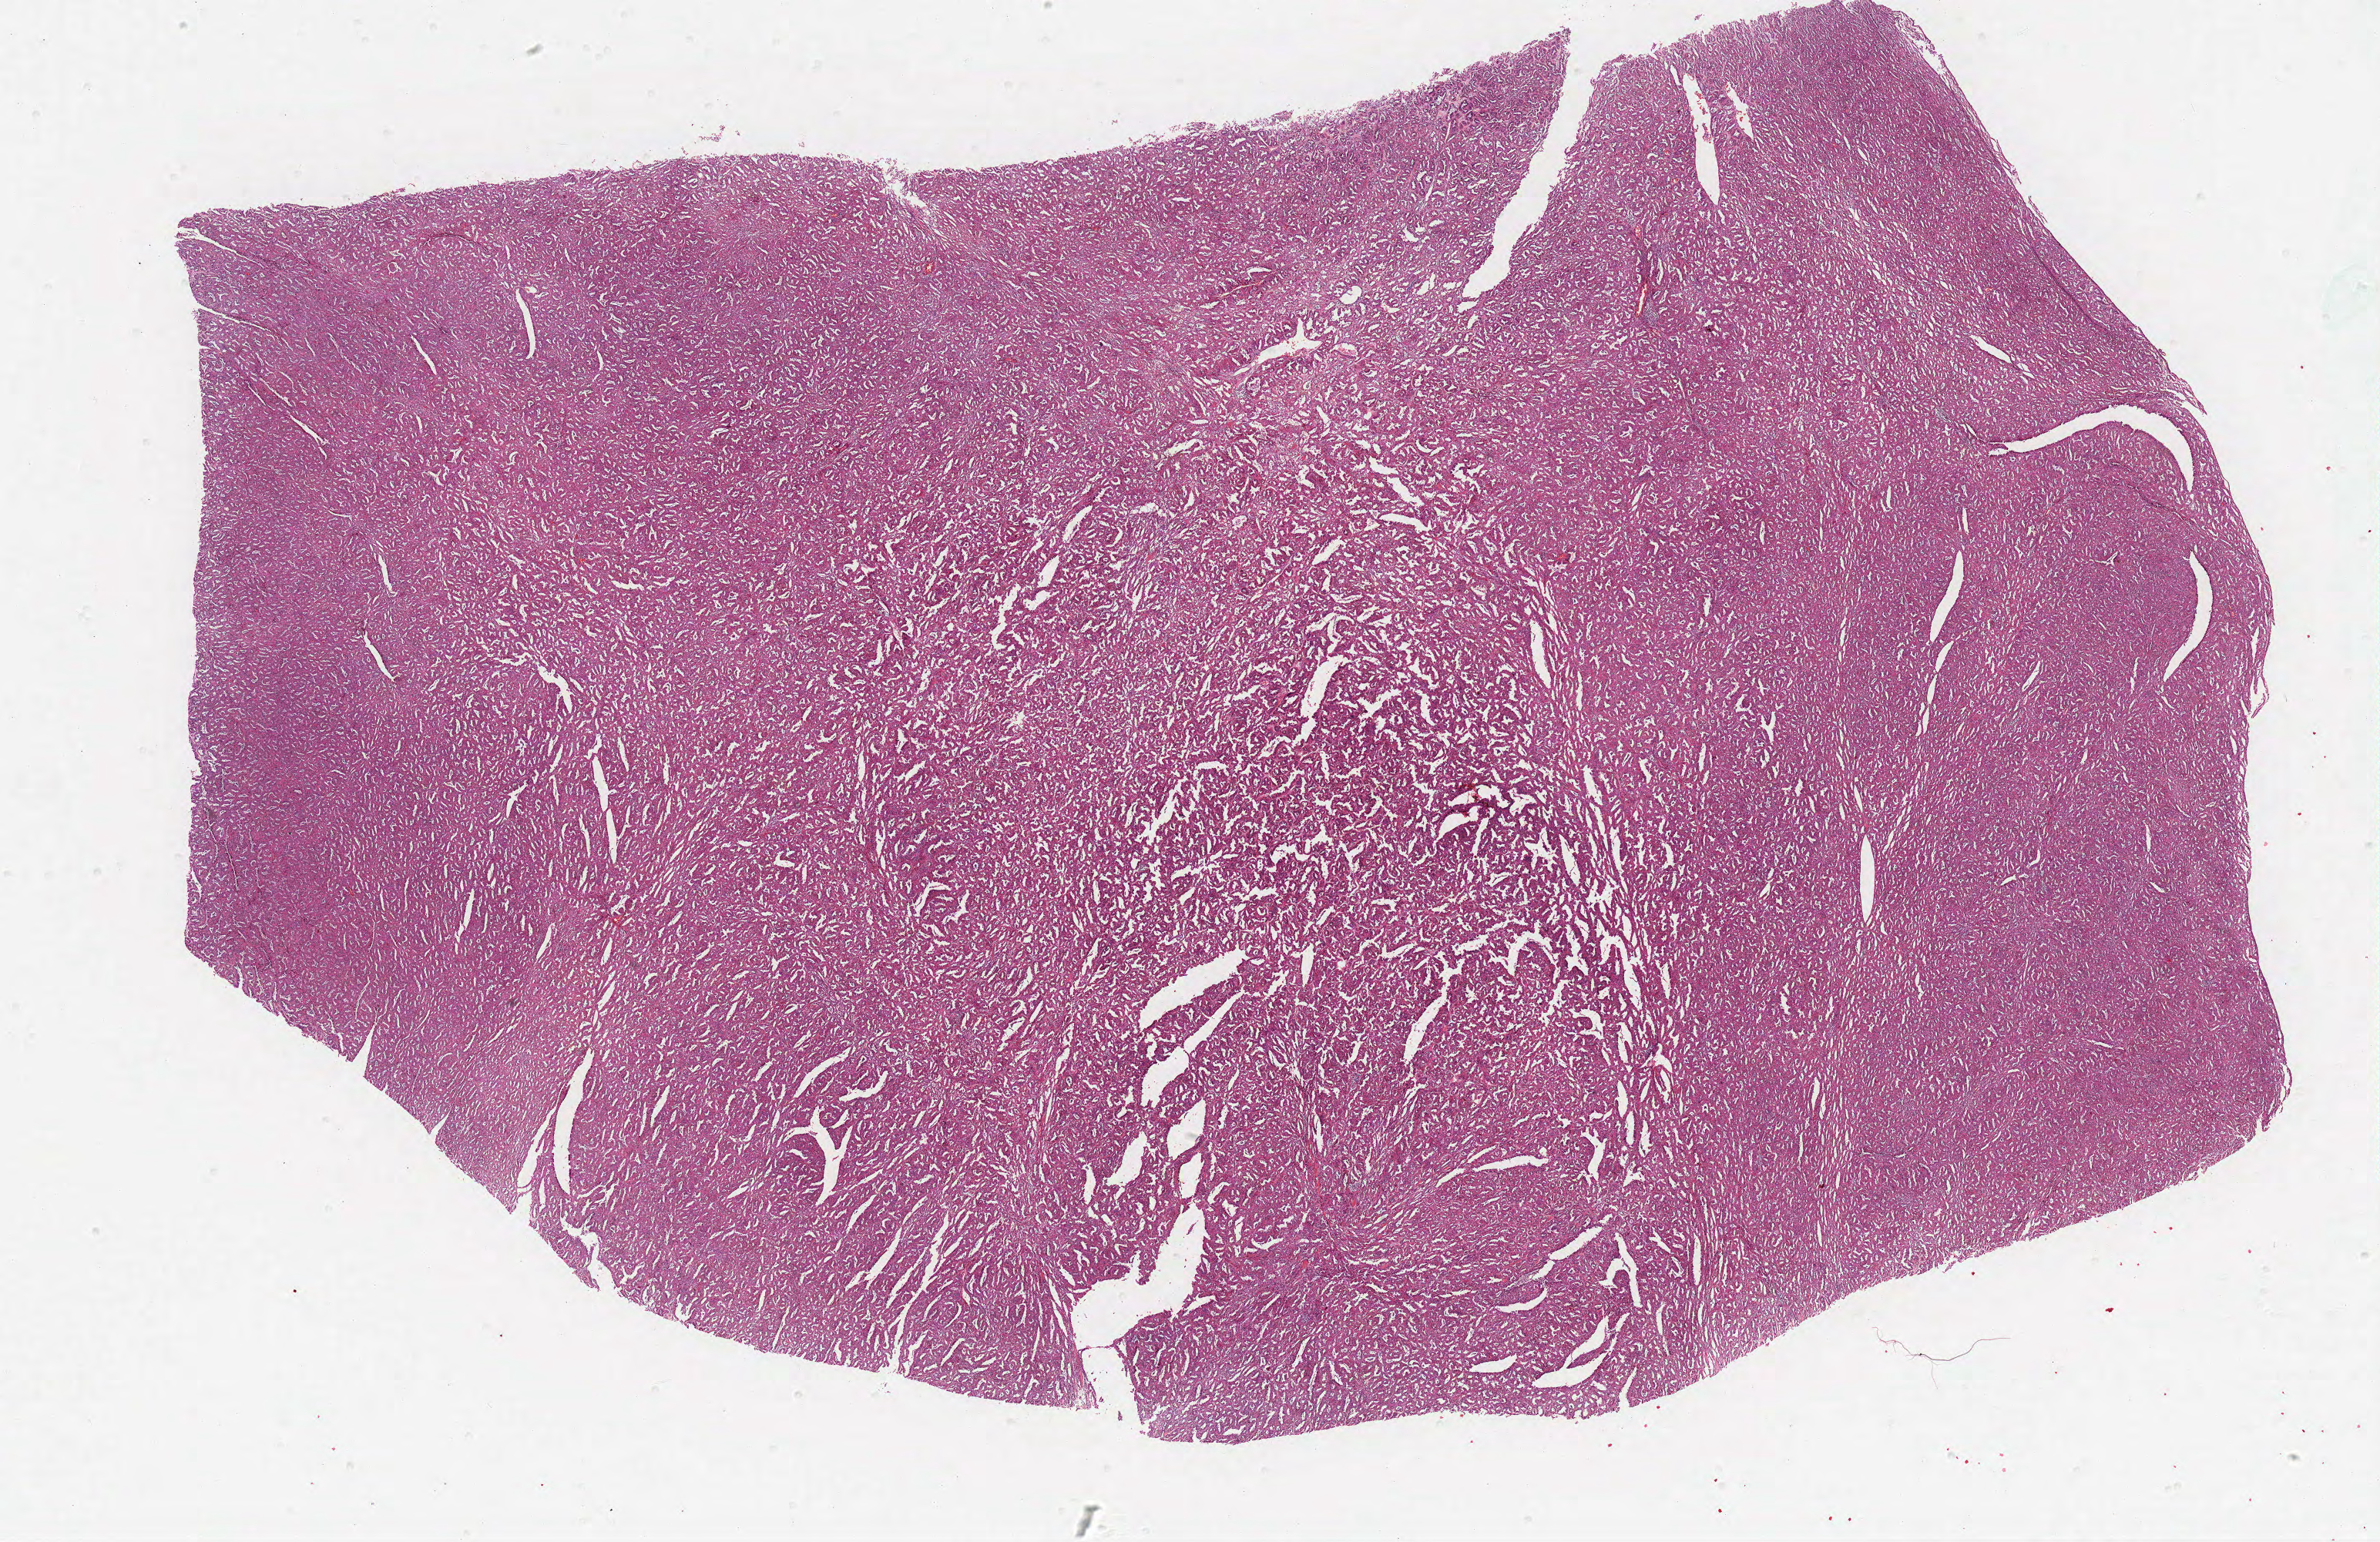
Whole-slide histology image, Hematoxylin and eosin (H&E) stained, whole scanned area (about 24.7 x 16.0 mm) shown as a low-resolution overview, FFPE section, primary tumour sample from the kidney. Male, age 63 years at initial diagnosis.
Histologic diagnosis: Papillary adenocarcinoma, NOS. Laterality: left. AJCC pathologic stage: III.